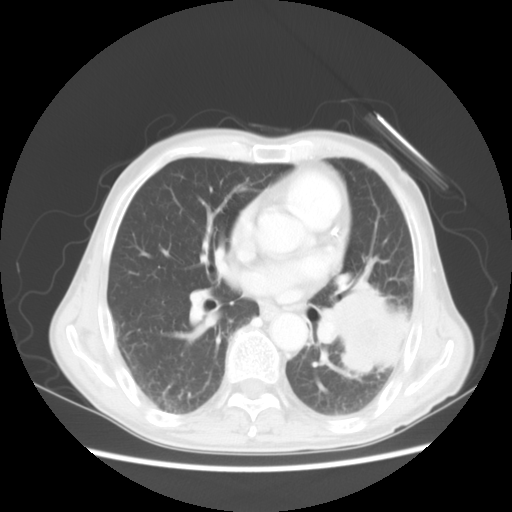
Chest CT, one axial slice; position 25 of 51 along the scan axis; 120 kVp; lung window (W 1500 / L -600 HU); 512 × 512 image matrix. Patient: male, 64 years. Case-level facts recorded for this patient, not image findings: clinical TNM (as recorded): T4 N0 M0; histopathological grade: G2-3.
Outlined on this slice (rectangle marked by the reading radiologist):
- lung tumour (recorded histology: squamous cell carcinoma): box from (x=316, y=280) to (x=413, y=402) px